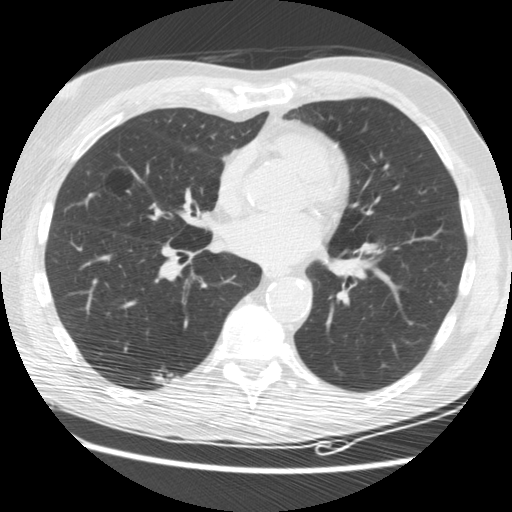
Low-dose screening chest CT, one axial slice; lung window (W 1500 / L -600 HU); 2.5 mm slice thickness; 512 × 512 image matrix, field of view 347 × 347 mm.
Outlined on this slice (outlined manually by an expert reader):
- lesion 2 (tumor, lower lobe of right lung): bounding box (x1, y1, x2, y2) in pixels: (152, 366, 177, 384)